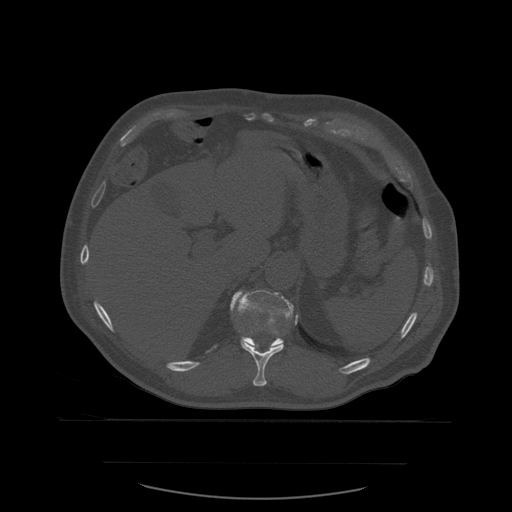
CT including the spine, one axial slice. Position 287 of 590 along the scan axis. Bone window (W 1800 / L 400 HU). 512 × 512 image matrix. Patient age 71 years. From the clinical record (not read from this slice): primary cancer: lung; vertebrae with lytic lesions (as recorded): T1, T2, L5, S1.
Outlined on this slice (semi-automatic segmentation, software-assisted and operator-edited):
- T11 vertebra: bounding box <240,315,298,387> (left, top, right, bottom; pixels)
- T12 vertebra: <230,290,299,350>